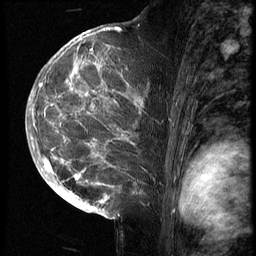
Breast MRI (dynamic contrast-enhanced), one sagittal slice. Position 39 of 70 along the scan axis. 3 images stored at this slice position (order not interpretable as contrast timing). 1.5 T. TE 4.2 ms, TR 9 ms. 256 × 256 image matrix, field of view 180 × 180 mm. Patient: female, 28 years. Case-level facts recorded for this patient, not image findings: setting: breast cancer imaged before/during neoadjuvant chemotherapy.
Structures marked on this image (semi-automatically segmented with operator editing):
- analysis volume of interest (the breast-tissue region the enhancement analysis was run in; not a lesion): box from (x=43, y=42) to (x=161, y=215) px
- tumour enhancement mask (voxels above the 140 % enhancement threshold inside the analysis volume of interest): (x=43, y=43)–(x=135, y=205)